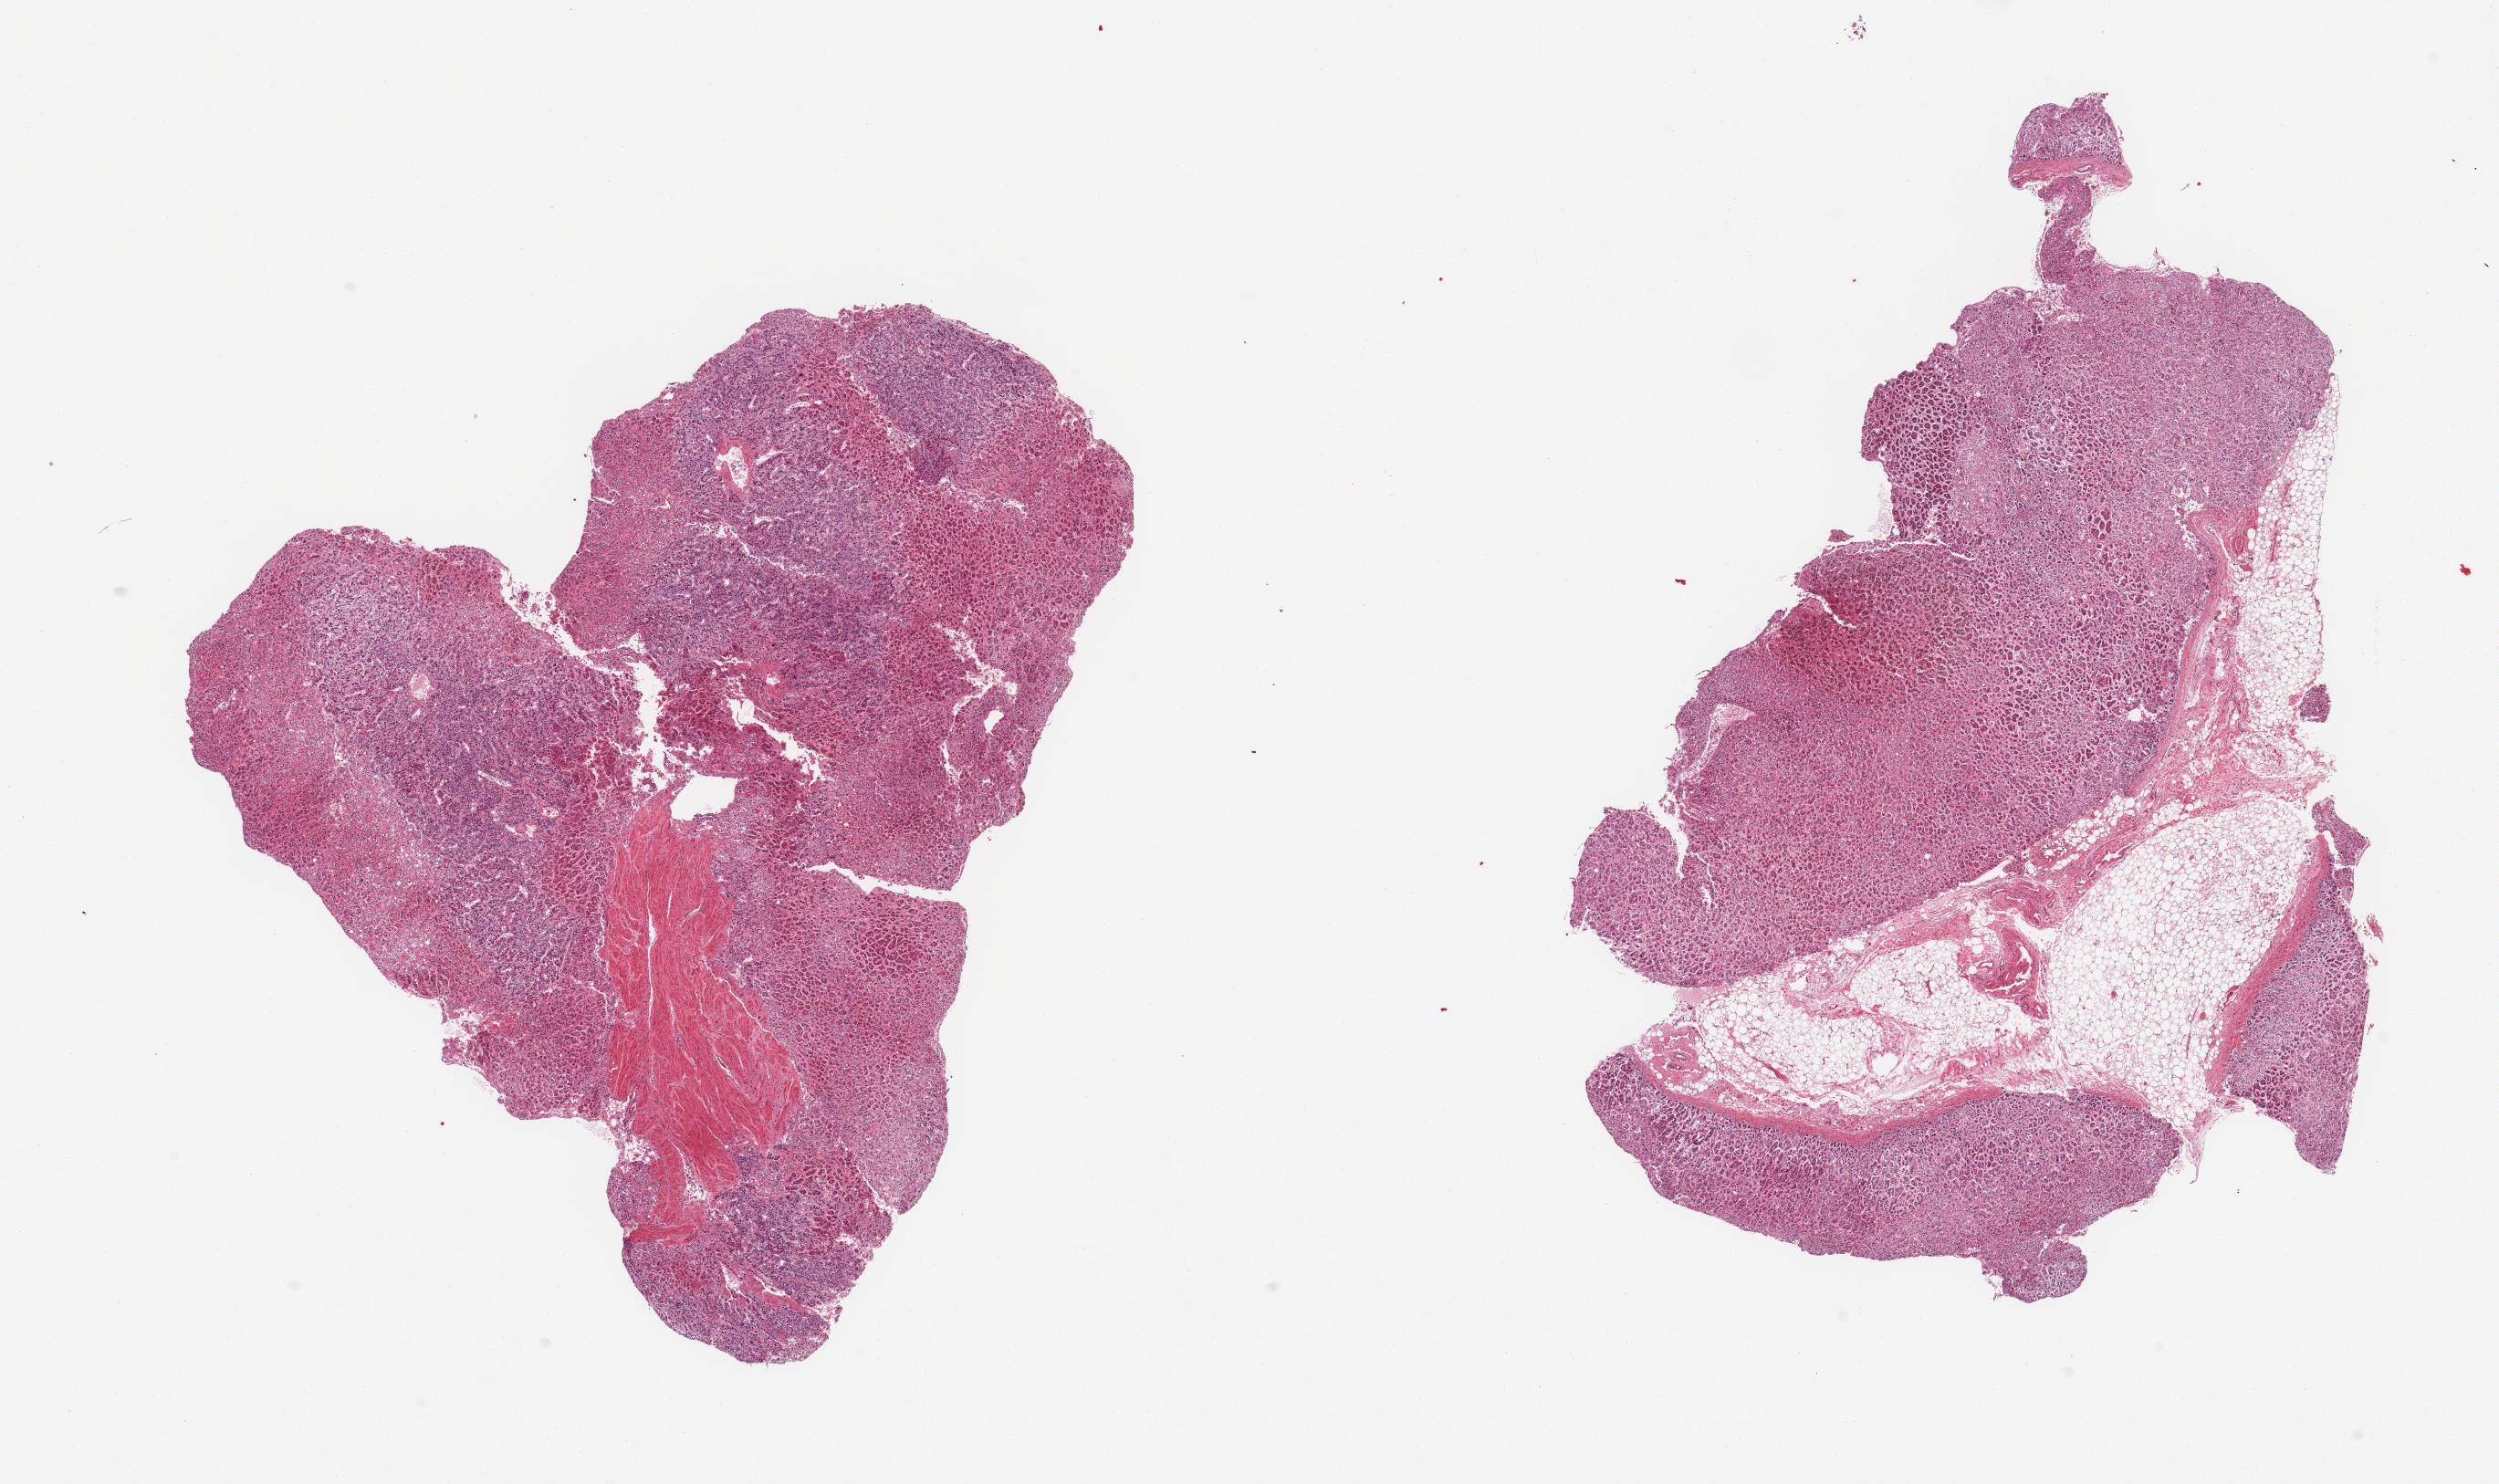
Digitized hematoxylin and eosin (H&E)-stained section — shown as a low-resolution overview of the whole scanned area (about 21.7 x 12.9 mm, slide scanned at 20x); PAXgene-fixed, paraffin-embedded tissue; section of adrenal gland (target tissue); tissue donor sample.
Reviewer comment on this tissue sample: 2 pieces; 1 has 40% internal fat; other has 10% internal fibromuscular, probably vascular, content.